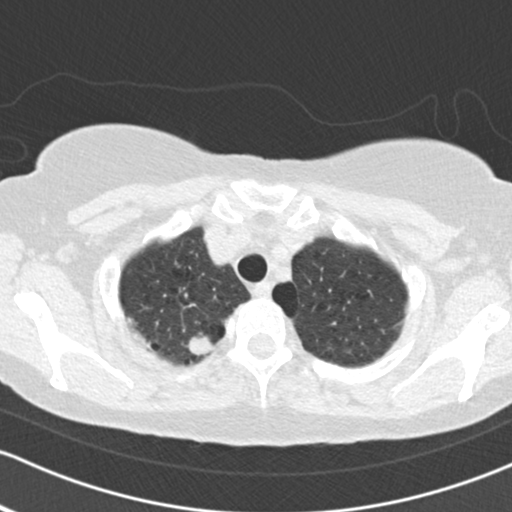
Axial slice from a low-dose chest CT screening exam; second screening round (one year after baseline); lung window (W 1500 / L -600 HU); standard (soft-tissue) reconstruction kernel (B30f); 120 kVp; slice 18 of 161 in the series. Female participant, aged 64 years at enrolment. Current smoker at enrolment.
- Expert reader's lesion annotation, box from (x=172, y=324) to (x=221, y=369) px.
- Reader record for this screening exam (exam-level; its link to the box is not recorded): non-calcified nodule or mass ≥4 mm, right upper lobe, 16 × 15 mm, spiculated (stellate) margins, soft tissue attenuation, pre-existing on the prior screen: no.